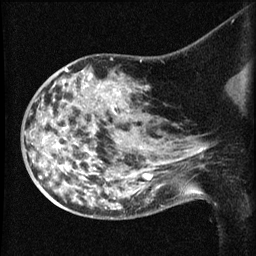
Breast MRI (dynamic contrast-enhanced), one sagittal slice; position 36 of 60 along the scan axis; dynamic contrast-enhanced series, image 2 of 3 at this slice position (ordered by acquisition); 1.5 T; TE 4.2 ms, TR 8.2 ms; 2.1 mm slice thickness; 256 × 256 image matrix. Female patient, age 50 years.
Annotated regions visible in this slice (semi-automatically segmented with operator editing):
- analysis volume of interest (the breast-tissue region the enhancement analysis was run in; not a lesion): bounding box [x1, y1, x2, y2] px = [38, 74, 169, 211]
- tumour enhancement mask (voxels above the 70 % enhancement threshold inside the analysis volume of interest): [40, 174, 147, 179]